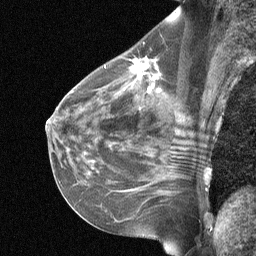
Breast MRI (dynamic contrast-enhanced), one sagittal slice; slice 36 of 64 in the series (ordered by position); dynamic contrast-enhanced study with each time point stored as its own series, time point 2 of 3 at this slice position (early post-contrast, ordered by acquisition time); 1.5 T; TE 4.8 ms, TR 27 ms; 2 mm slice thickness; 256 × 256 image matrix, field of view 200 × 200 mm. Female patient, age 51 years. Case-level facts recorded for this patient, not image findings: setting: breast cancer imaged before/during neoadjuvant chemotherapy; receptor status: HR-positive, HER2-negative.
Outlined on this slice (semi-automatically segmented with operator editing):
- analysis volume of interest (the breast-tissue region the enhancement analysis was run in; not a lesion): box from (x=88, y=42) to (x=192, y=119) px
- tumour enhancement mask (voxels above the 90 % enhancement threshold inside the analysis volume of interest): (x=132, y=58)–(x=157, y=92)